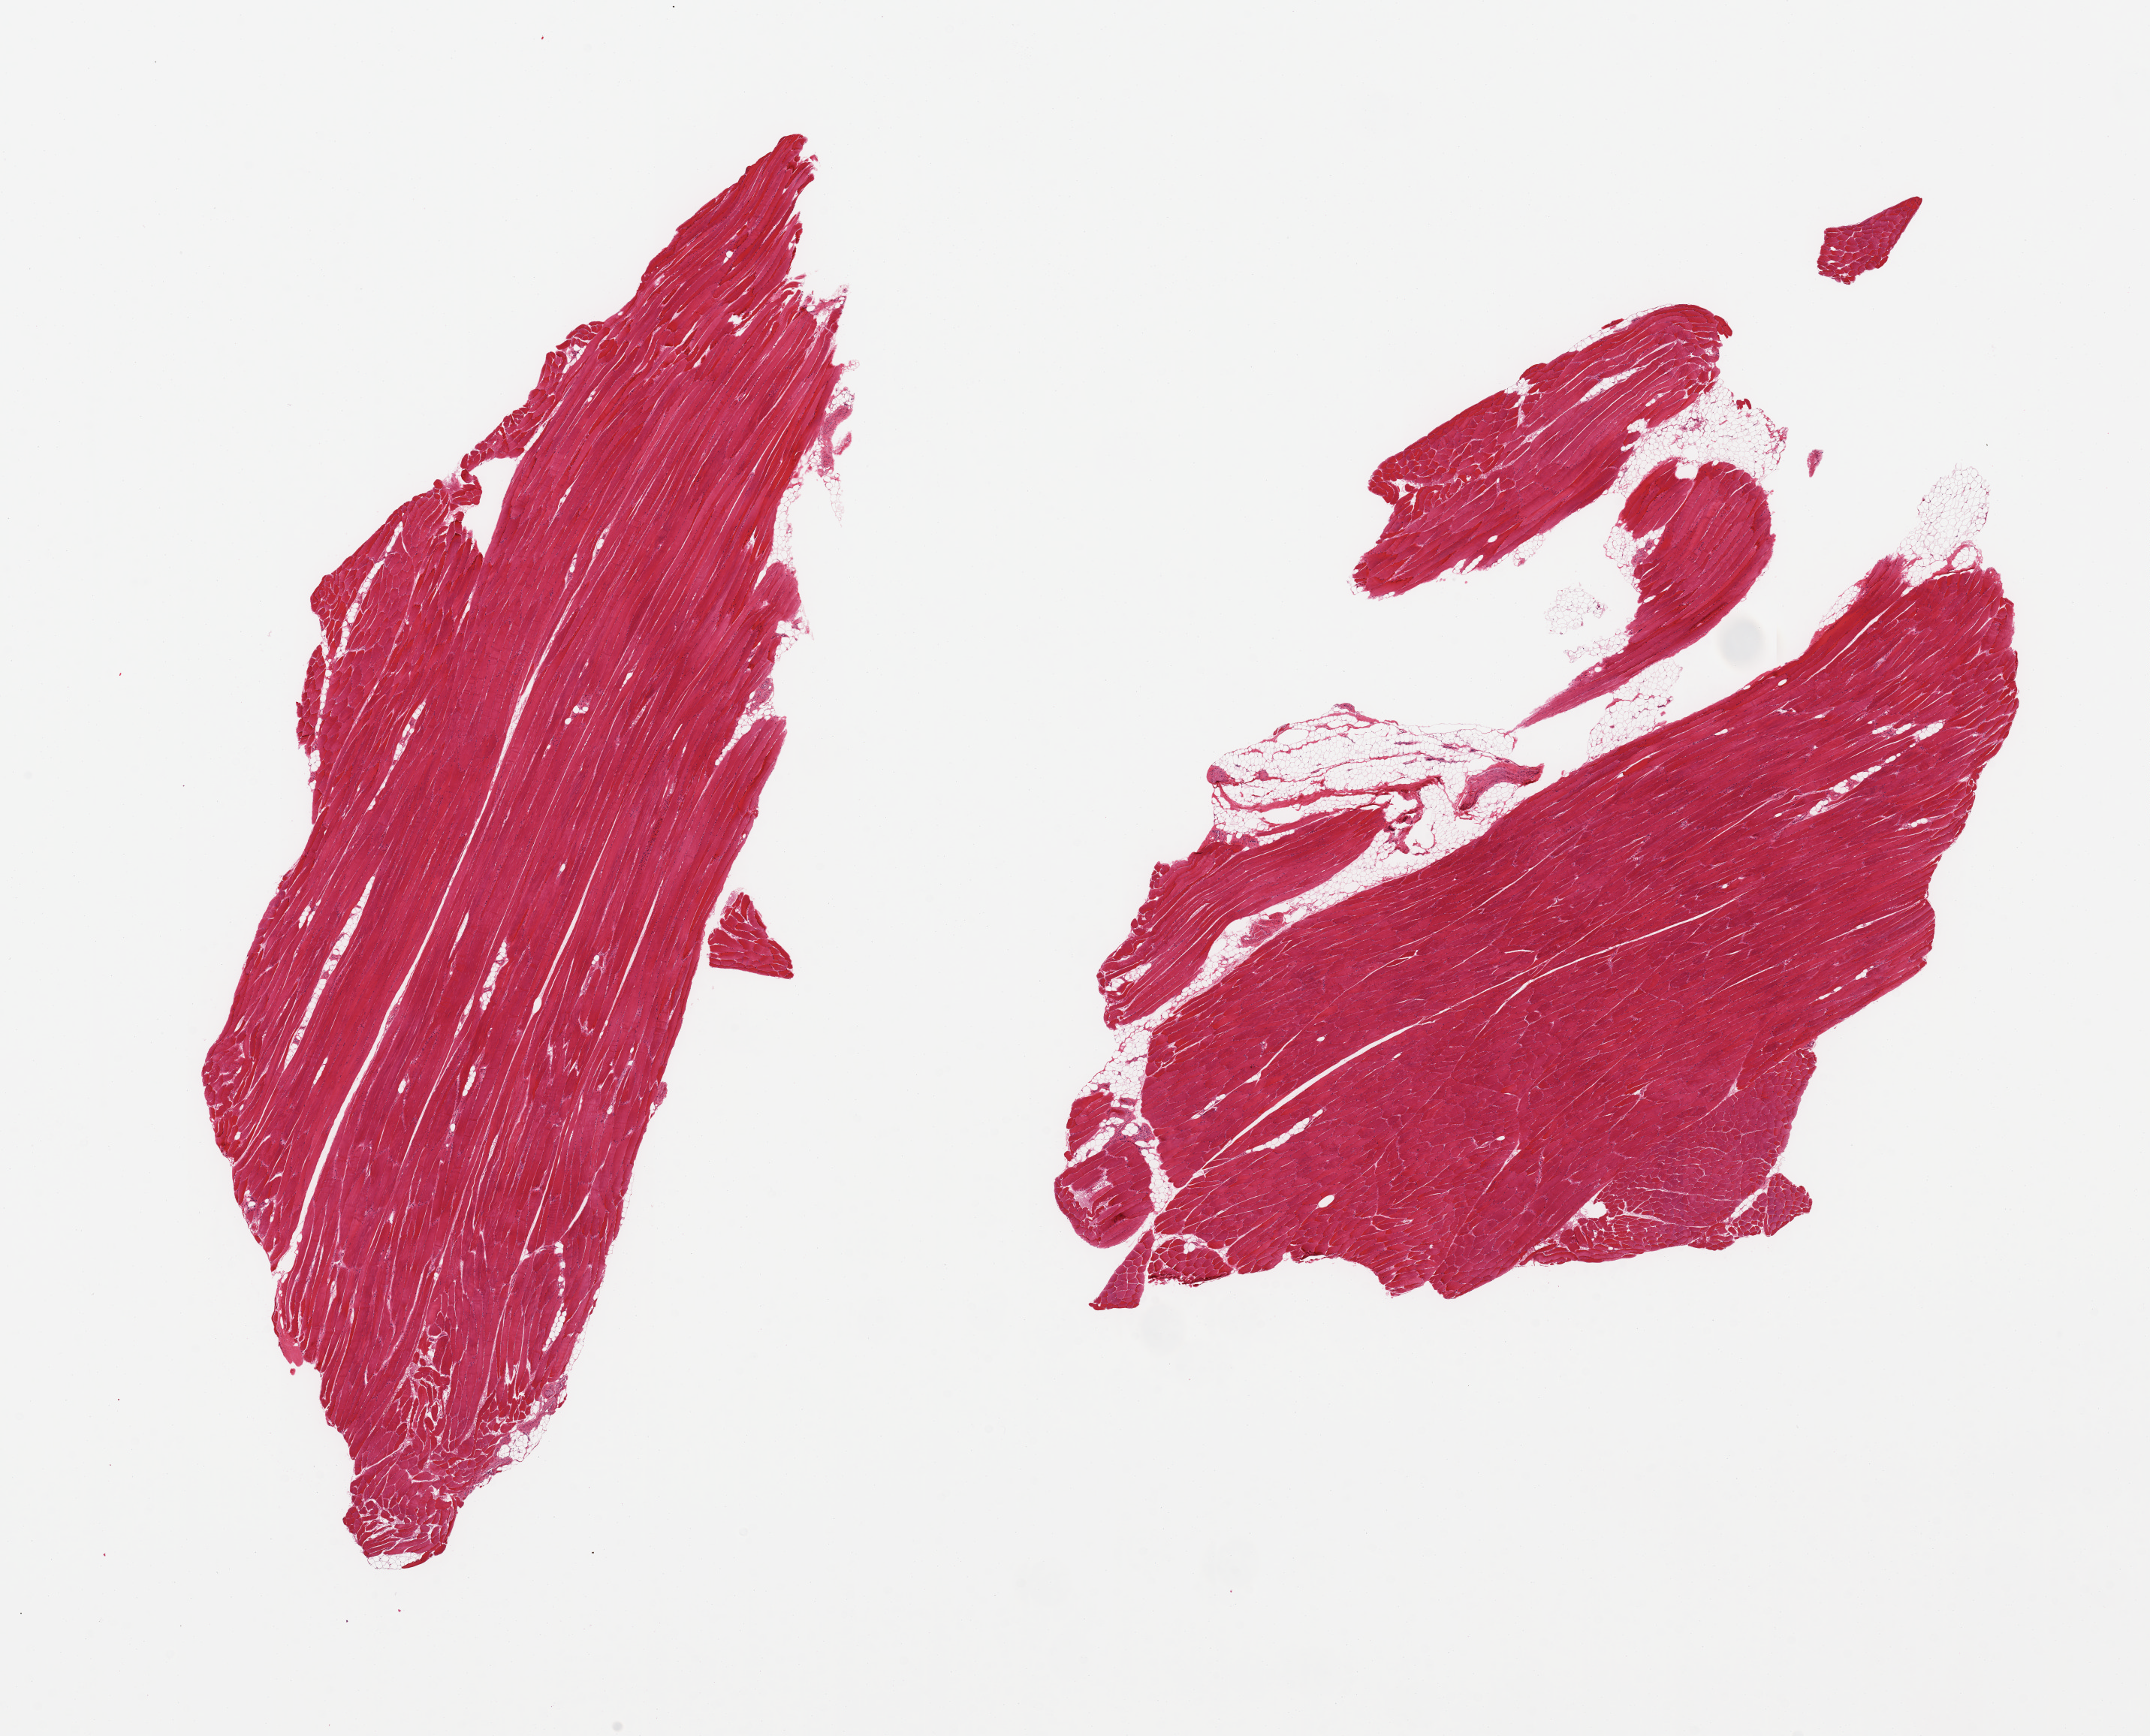
Digitized haematoxylin and eosin-stained section — low-resolution overview of the scanned area, about 22.6 x 18.3 mm; PAXgene-fixed paraffin-embedded (PFPE) section; target tissue: skeletal muscle; donor tissue sample. Donor: male.
Reviewer comment on this tissue sample: 2 pieces; 10% fat in 1 fragmented piece.